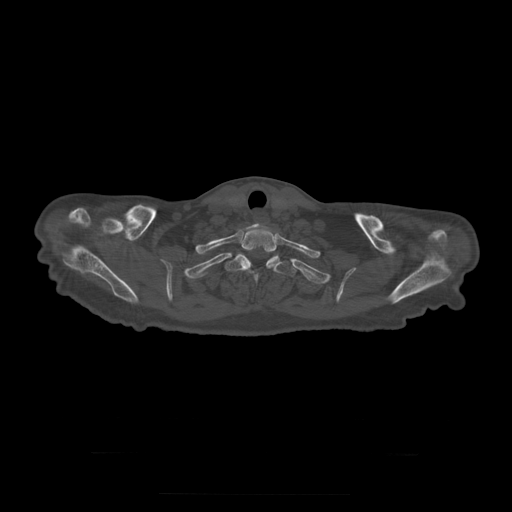
CT including the spine, one axial slice; slice 281 of 397 in the series (ordered by position); 120 kVp; bone window (W 1800 / L 400 HU); 1.25 mm slice thickness; 512 × 512 image matrix, field of view 510 × 510 mm. Patient age 73 years. Case-level facts recorded for this patient, not image findings: primary cancer: prostate.
Structures marked on this image (semi-automatic segmentation, software-assisted and operator-edited):
- T1 vertebra: bounding box (x1, y1, x2, y2) in pixels: (238, 231, 276, 264)
- T2 vertebra: (225, 255, 297, 286)